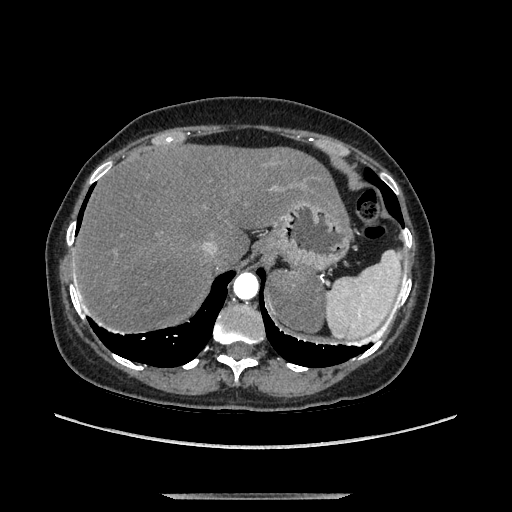
Contrast-enhanced abdominal CT, one axial slice. Slice 111 of 169 in the series (ordered by position). Soft-tissue window (W 400 / L 40 HU). 512 × 512 image matrix. Female patient. Case-level facts recorded for this patient, not image findings: diagnosis: adrenocortical carcinoma; tumour side: left adrenal; tumour size at pathology: 9 cm; Ki-67 index: 2 %; stage (as recorded): 3.
Annotated regions visible in this slice (semi-automatic segmentation, software-assisted and operator-edited):
- mass: bounding box (x1, y1, x2, y2) in pixels: (271, 274, 324, 330)